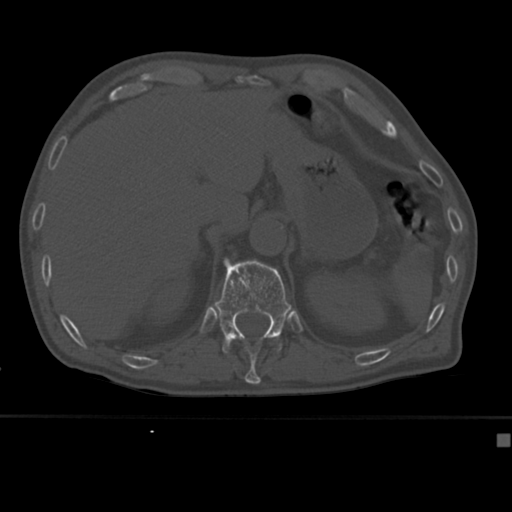
CT including the spine, one axial slice. Position 196 of 430 along the scan axis. Bone window (W 1800 / L 400 HU). 512 × 512 image matrix, field of view 337 × 337 mm. Male patient, age 64 years. Case-level facts recorded for this patient, not image findings: primary cancer: uterus; vertebrae with lytic lesions (as recorded): T1, T4, T5, T7, L5.
Annotated regions visible in this slice (semi-automatic segmentation, software-assisted and operator-edited):
- T11 vertebra: bounding box [x1, y1, x2, y2] px = [244, 350, 261, 382]
- T12 vertebra: [214, 258, 292, 354]